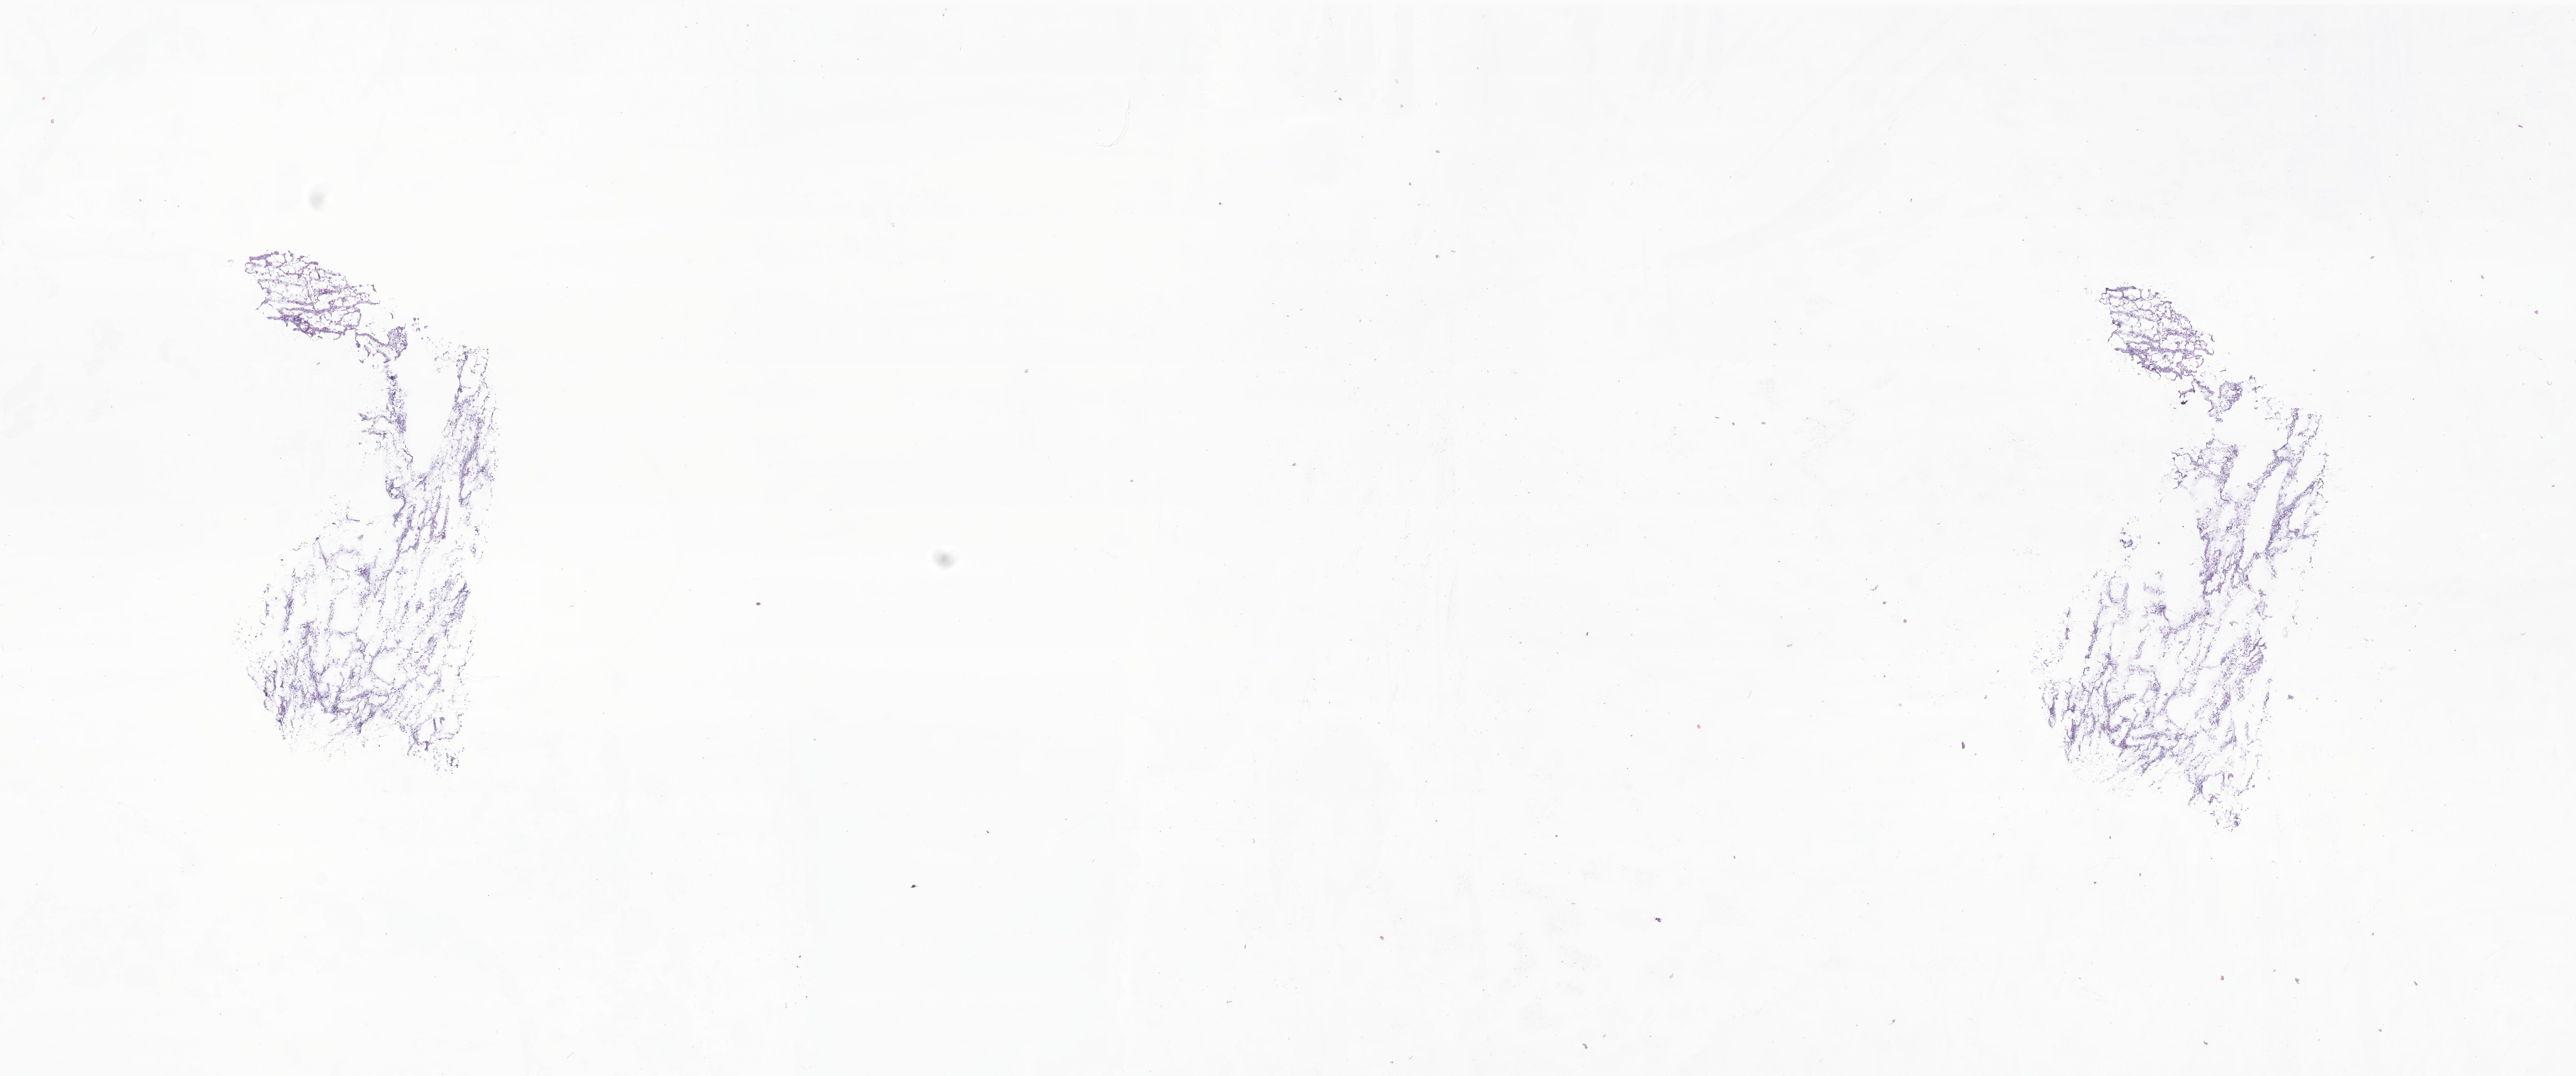
Digitized haematoxylin and eosin-stained section of tumor tissue from the orbit — a low-resolution overview of the entire scanned area, about 19.1 x 8.0 mm. Cryosection (OCT / tissue freezing medium). Patient: male, age 56 months (4 years 8 months).
Diagnosis (ICD-O-3 morphology term): Embryonal rhabdomyosarcoma, NOS.